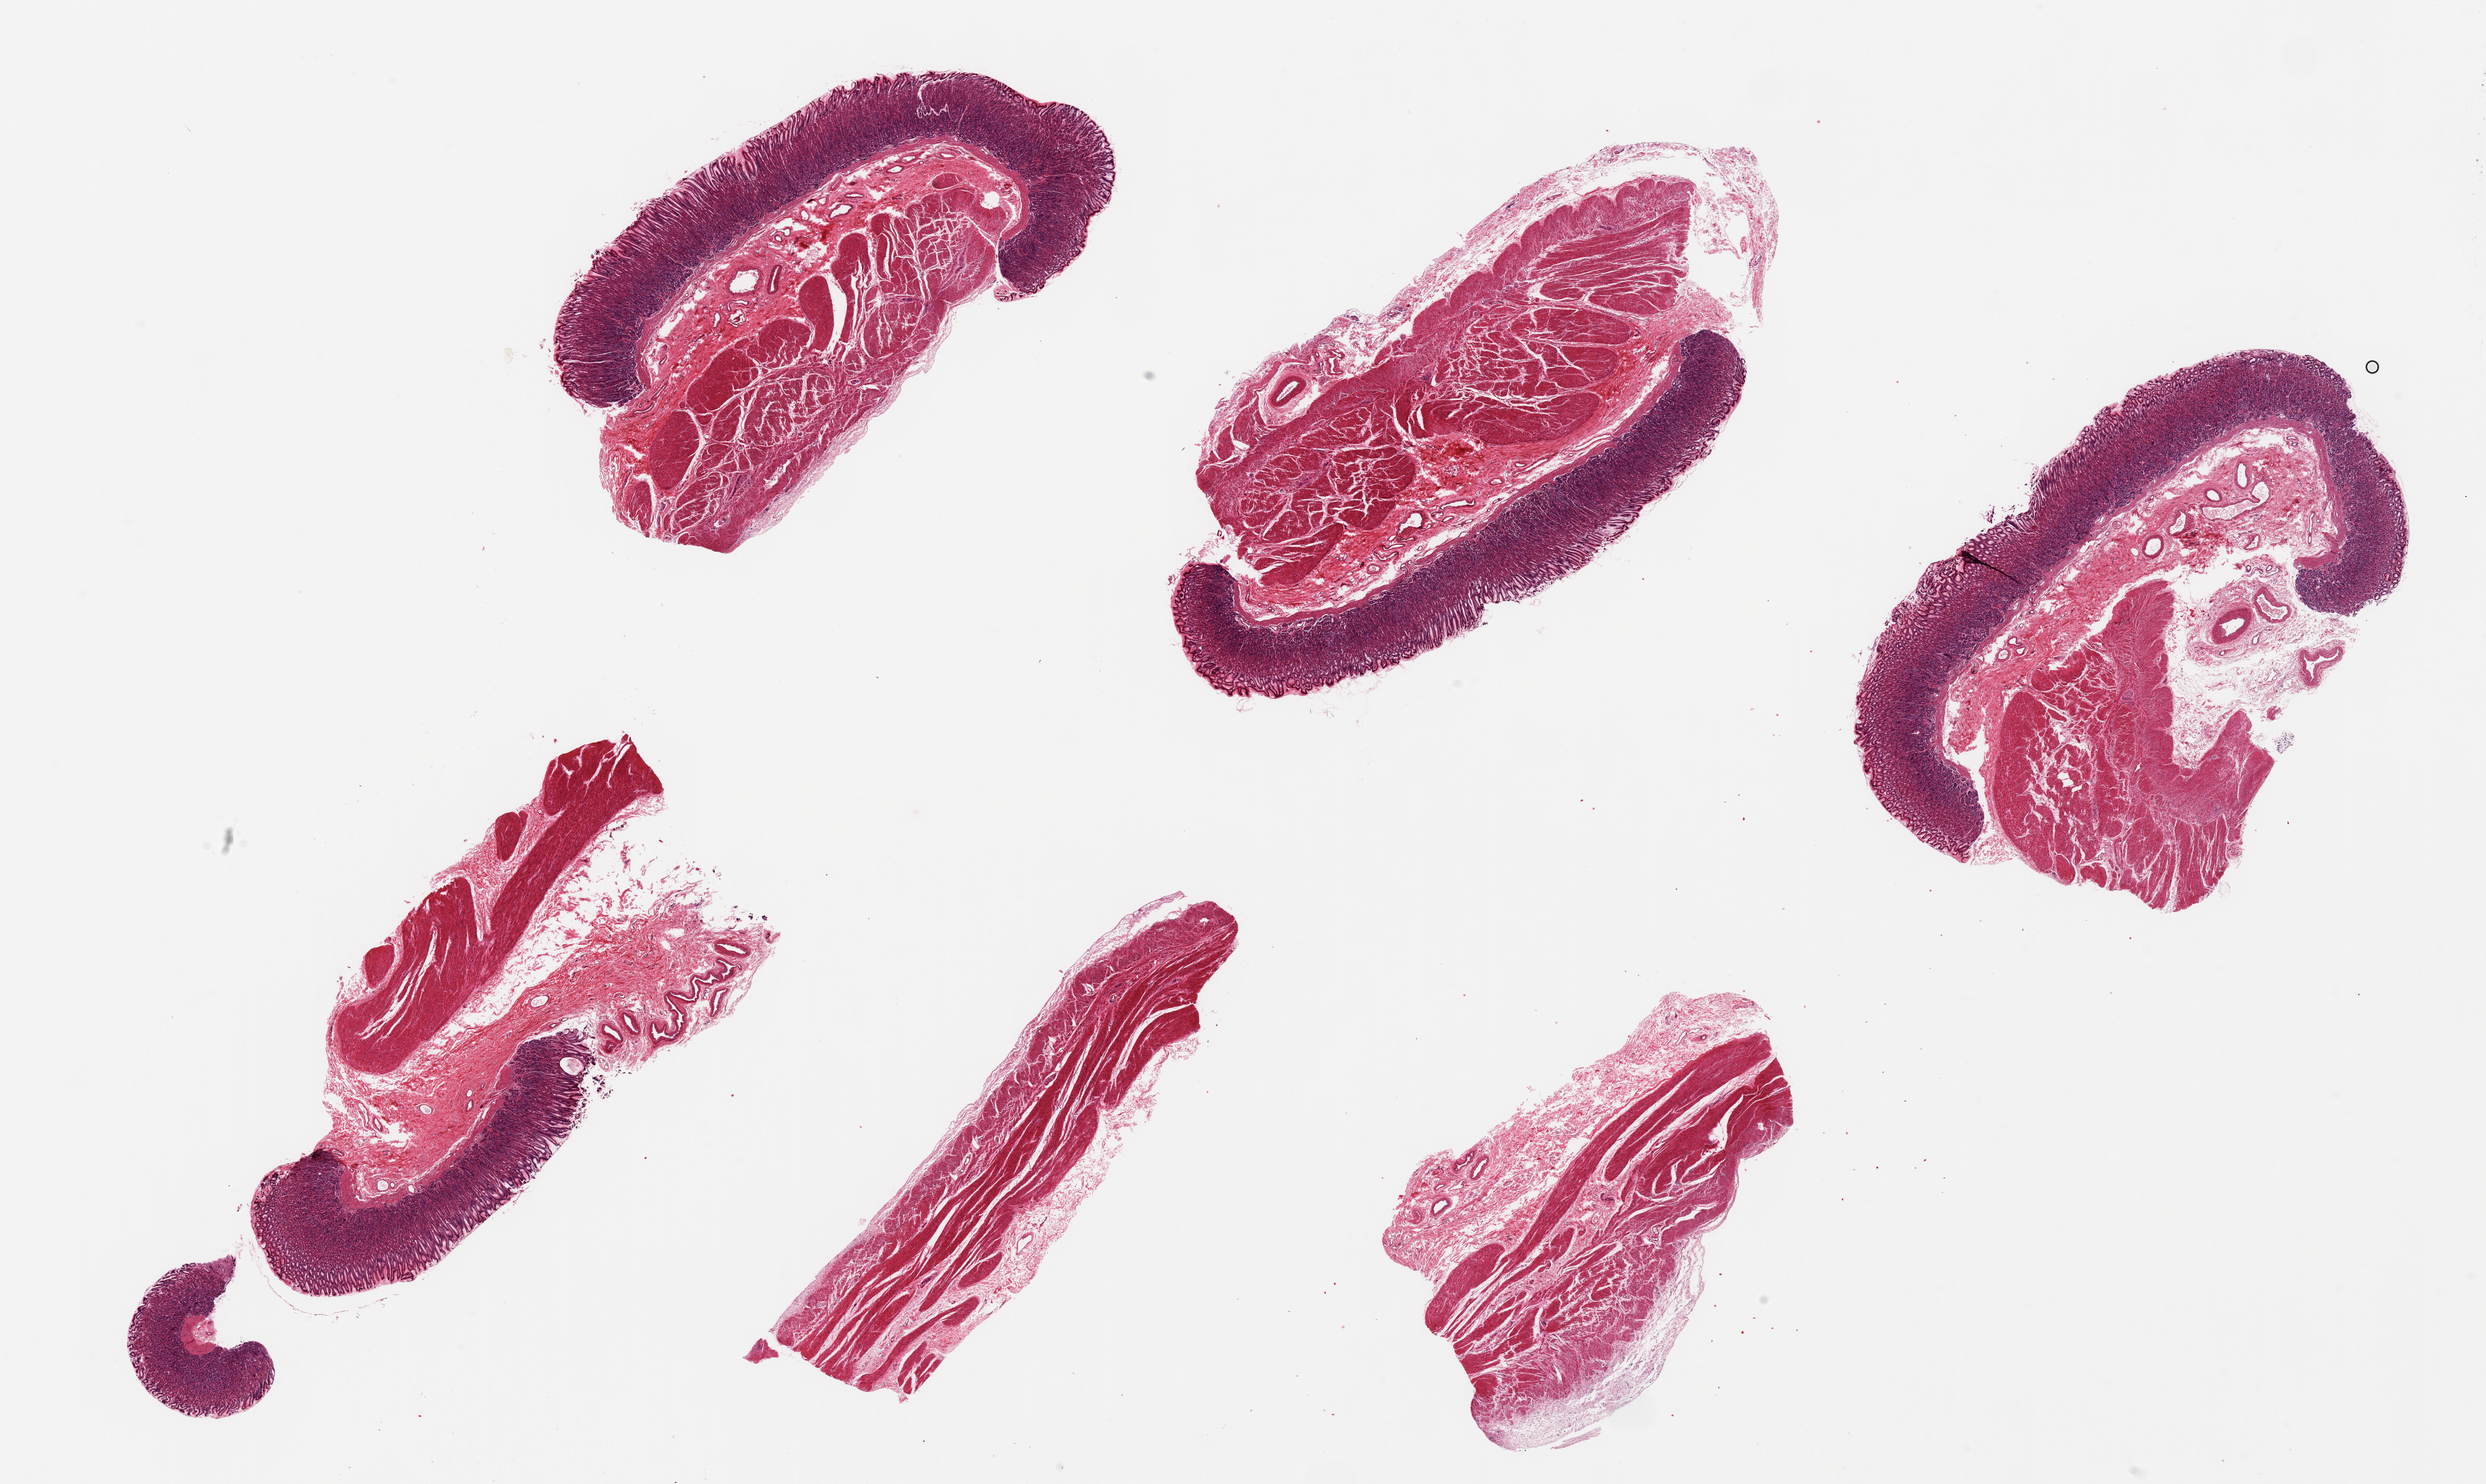
Hematoxylin and eosin (H&E) whole-slide image, whole scanned area (about 31.5 x 18.8 mm) shown as a low-resolution overview; PAXgene-fixed paraffin-embedded (PFPE) section; section of stomach (target tissue); tissue donor sample.
Review note (as recorded): 6 pieces ~8x4mm, mucosa well preserved, 20-40% of thickness.